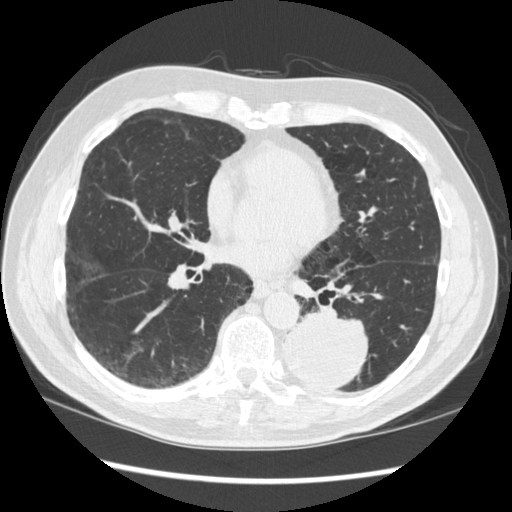
Low-dose screening chest CT, one axial slice; slice 147 of 348 in the series (ordered by position); reconstruction kernel STANDARD; lung window (W 1500 / L -600 HU); 1.25 mm slice thickness; 512 × 512 image matrix.
Structures marked on this image (expert manual segmentation):
- lesion 1 (tumor, lower lobe of left lung): bounding box <283,312,369,390> (left, top, right, bottom; pixels)